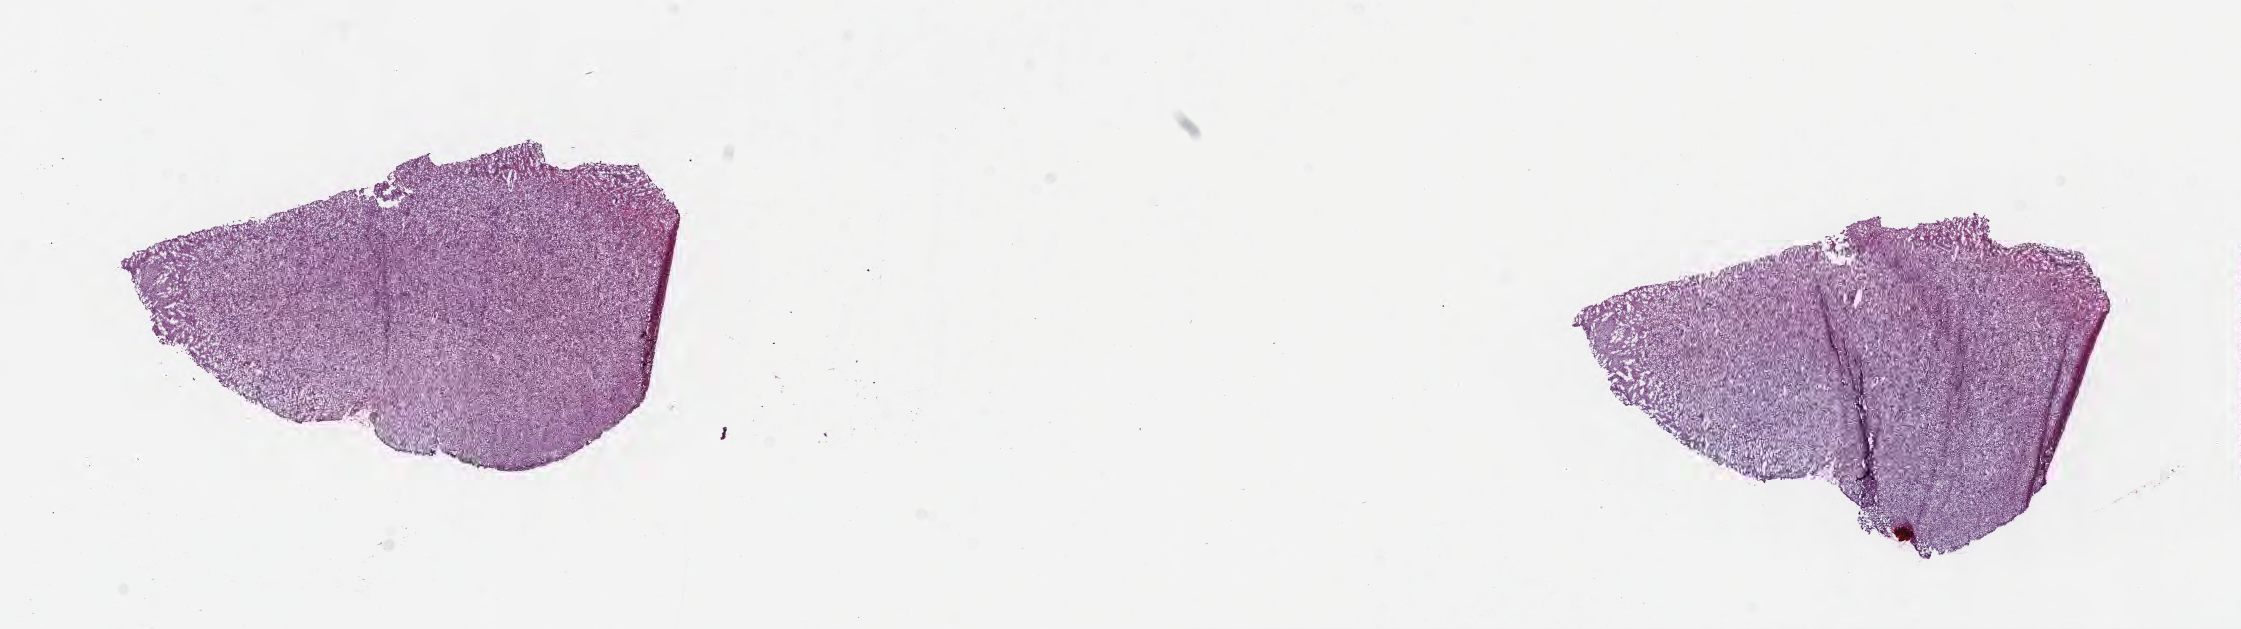
Whole-slide image, H&E stain — a low-resolution overview of the entire scanned area, about 18.1 x 5.1 mm. Frozen section. Specimen: recurrent tumor. Anatomic site: brain. Patient: male, age at initial diagnosis 66 years. Pathologist review of this section (percent, as recorded): tumor cells 15%, tumor nuclei 50%, stromal cells 70%, necrosis 0%, normal cells 15%. Inflammatory infiltration, as recorded: lymphocyte infiltration 0%, monocyte infiltration 0%, neutrophil infiltration 0%.
* patient diagnosis: Glioblastoma, NOS